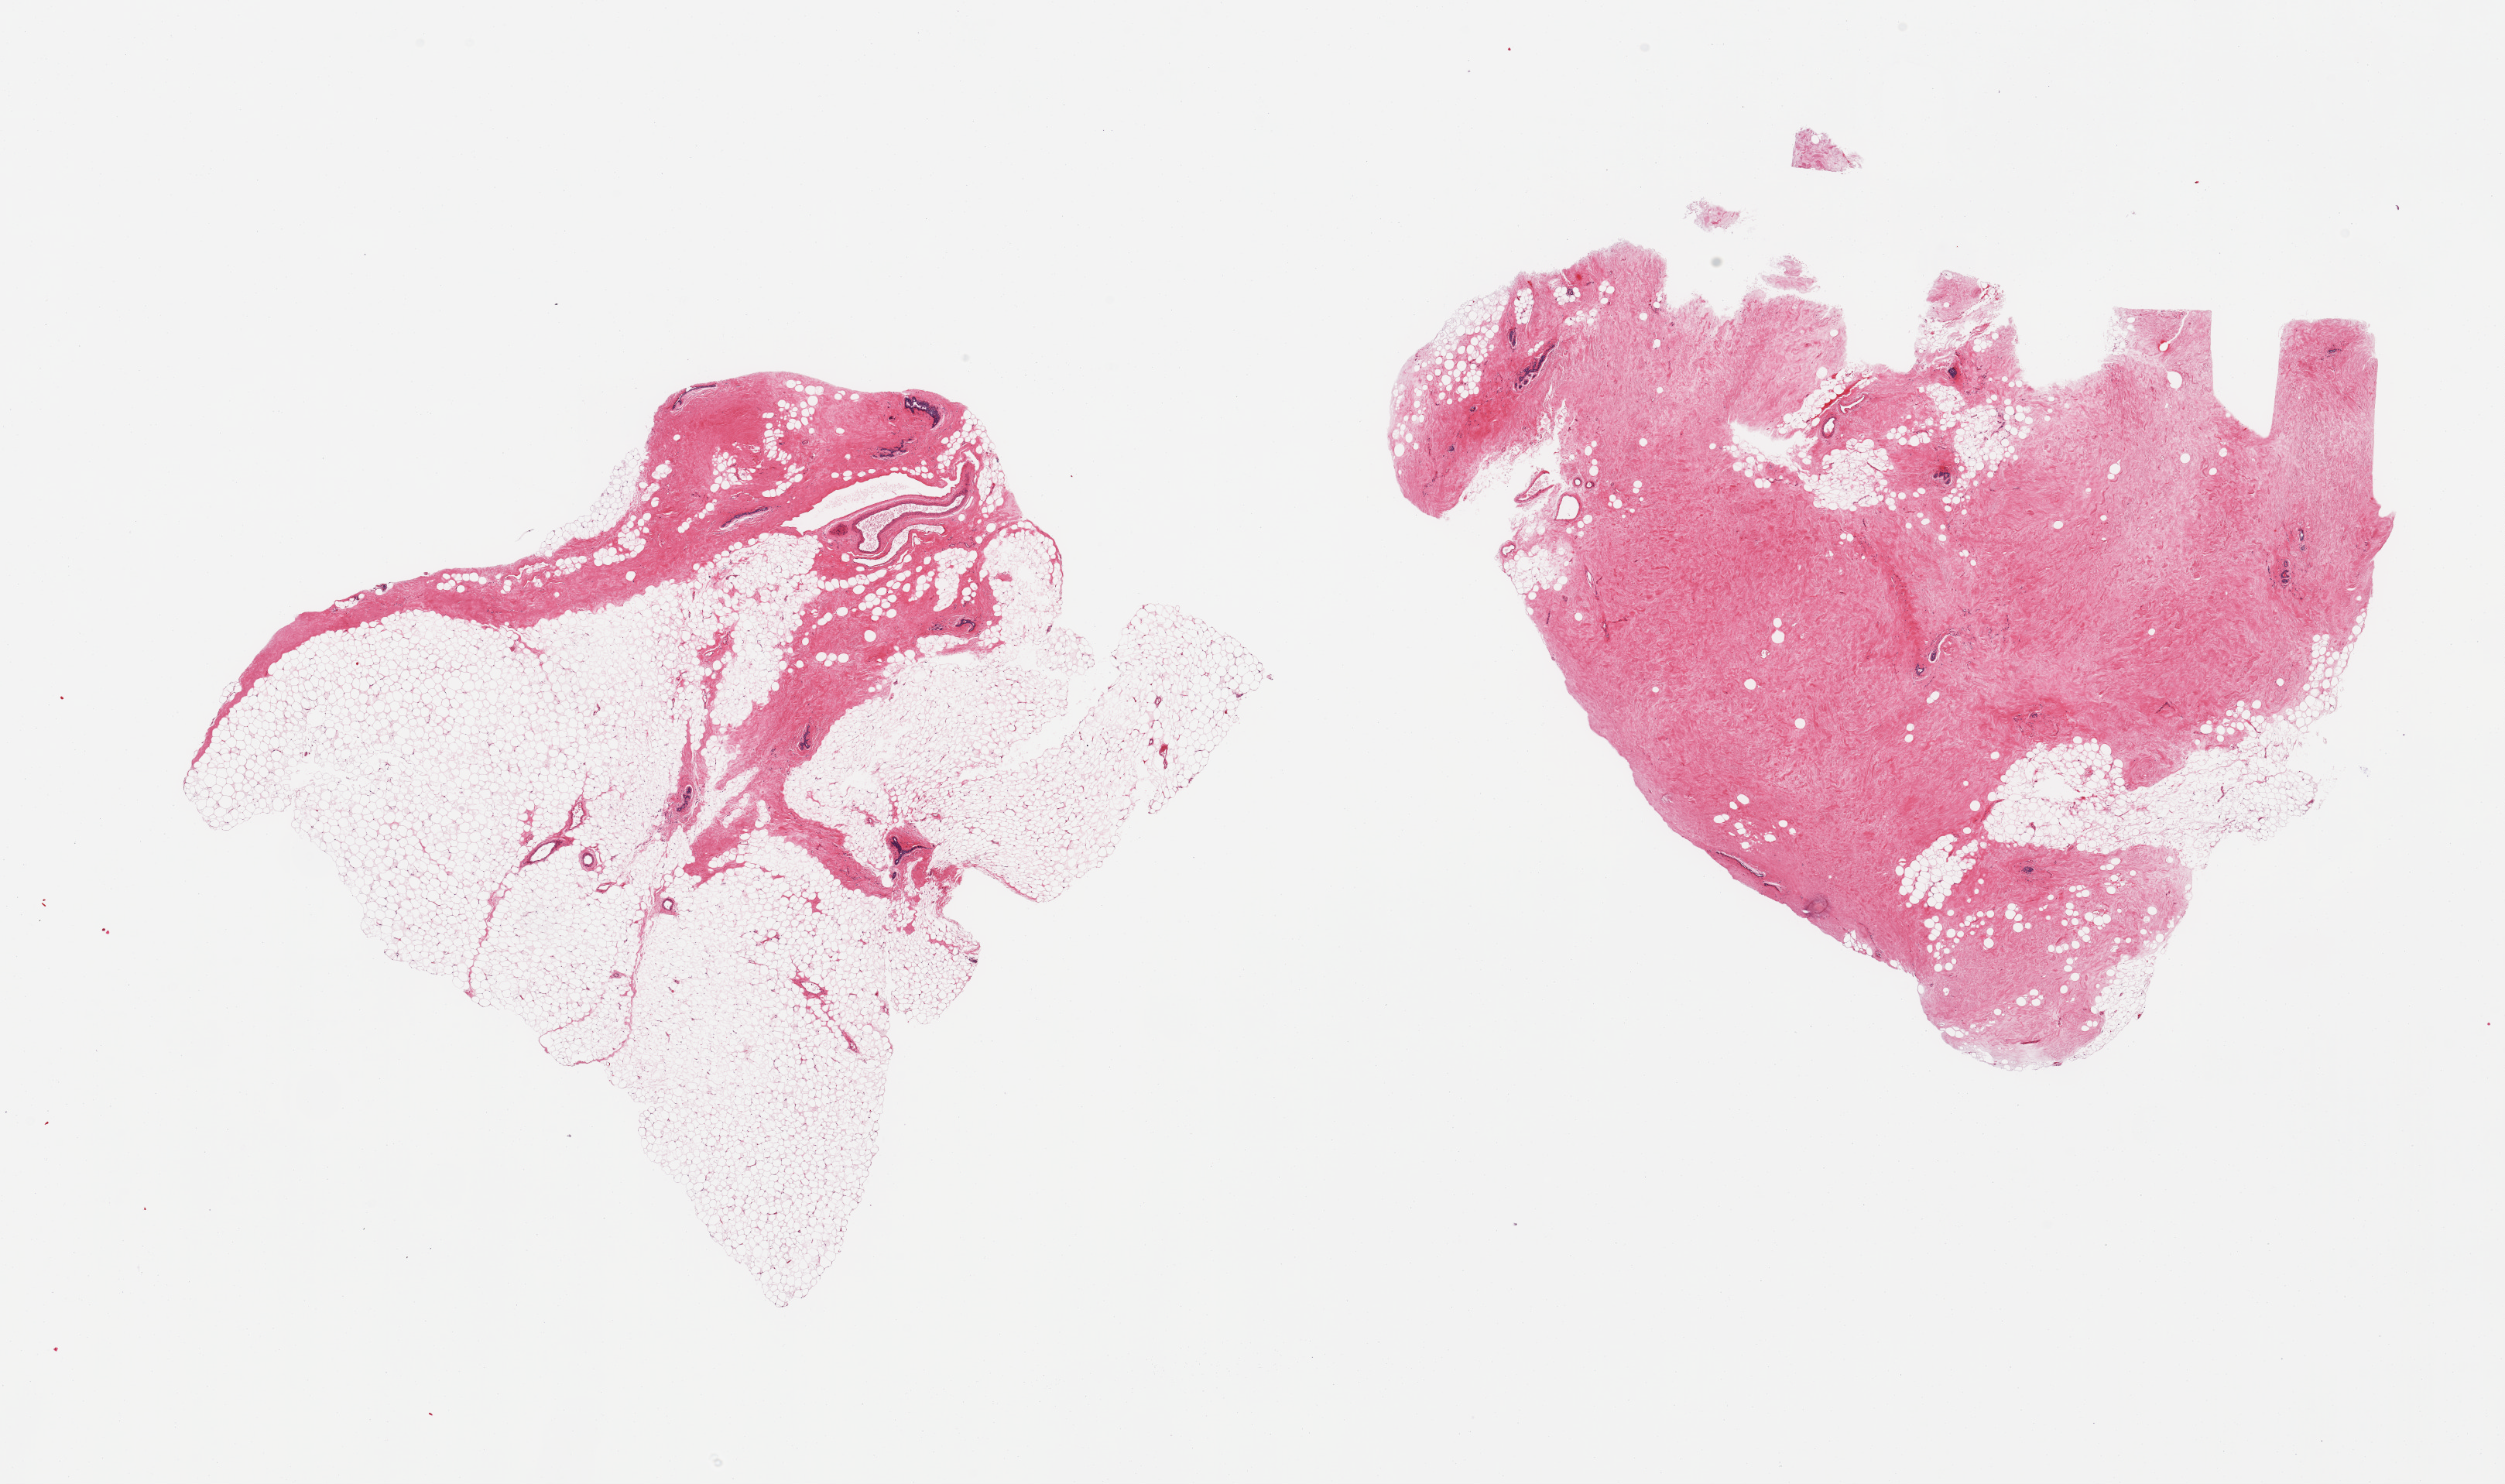
Hematoxylin and eosin (H&E) whole-slide image — low-resolution overview of the scanned area, about 25.6 x 15.2 mm (slide scanned at 20x). PAXgene-fixed paraffin-embedded (PFPE) section. Section of breast (target tissue). Donor tissue sample. Donor sex: female.
Reviewer comment on this tissue sample: 2 pieces, mainly fibroadipose tissue; trace ductal/lobular units, storphic changes.